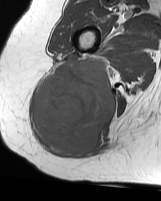
MRI of an extremity soft-tissue mass, one axial slice. Slice 34 of 70 in the series (ordered by position). MR volume resampled by the dataset authors to the PET/CT grid (not the native acquisition matrix). 161 × 201 image matrix, field of view 157 × 196 mm. Female patient. From the clinical record (not read from this slice): histological type: synovial sarcoma; grade: intermediate; site of the primary tumour: right buttock.
Structures marked on this image (expert contour drawn on MRI and transferred to this co-registered scan by the dataset authors):
- gross tumour volume including surrounding oedema: bounding box [x1, y1, x2, y2] px = [33, 56, 116, 155]
- gross tumour volume (mass): [33, 56, 116, 155]